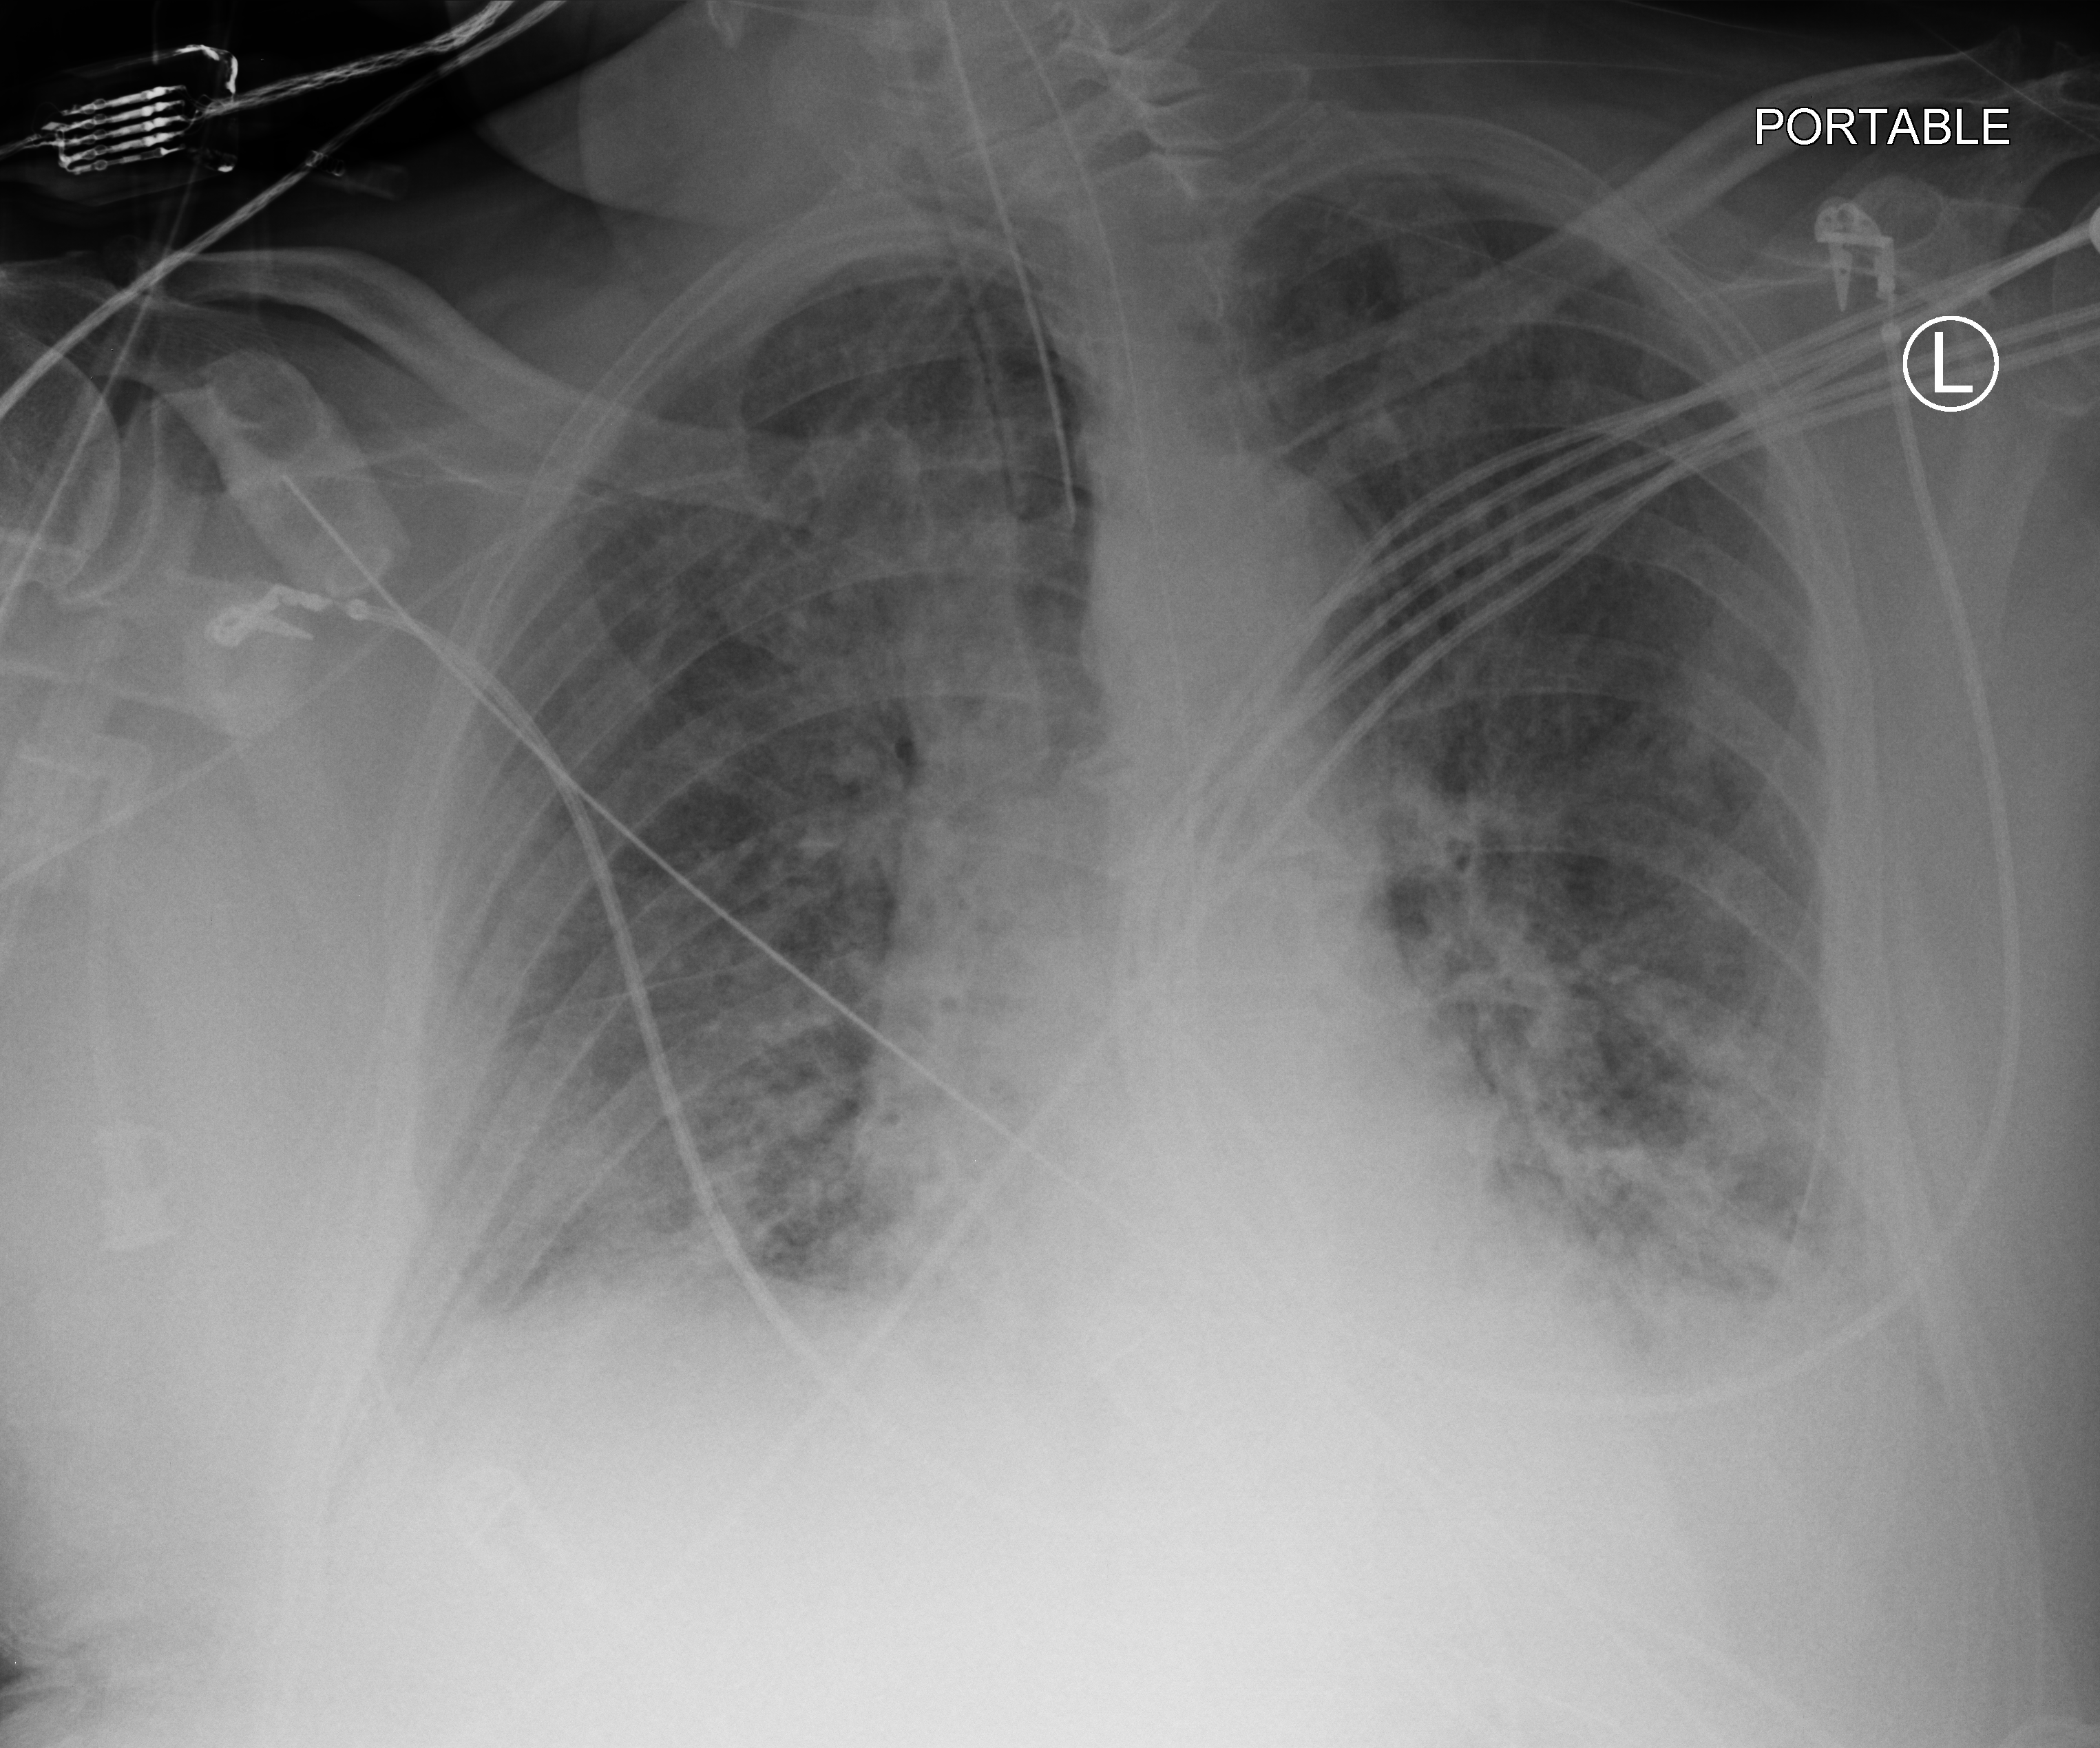
Bedside chest radiograph (computed radiography). Male patient hospitalised with COVID-19, age 60–74 years.
From the hospital-stay record, not from the radiograph (when in the stay this image was taken is not recorded):
- admitted to intensive care during this hospital stay: yes
- mechanically ventilated during this hospital stay: yes